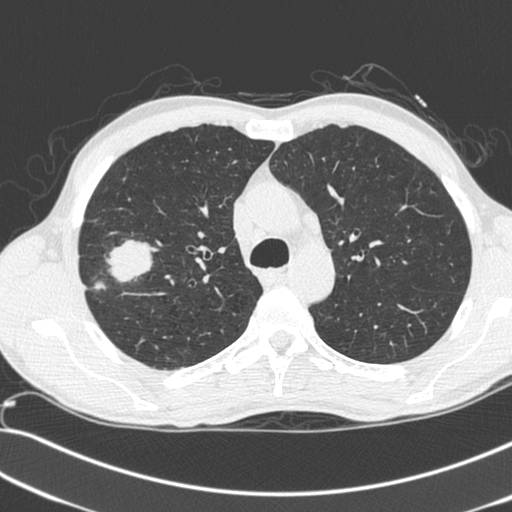
Axial slice from a low-dose chest CT screening exam; first (baseline) screen; lung window (W 1500 / L -600 HU); 1.3 mm slice thickness; standard (soft-tissue) reconstruction kernel (C); 120 kVp; 512 × 512 image matrix. Male, age 55 years at enrolment.
Expert-annotated lung lesion, bounding box [x1, y1, x2, y2] px = [72, 235, 151, 307]. The exam's reader record, not a measurement of the box and not confirmed to be the same lesion: non-calcified nodule or mass ≥4 mm, right upper lobe, 52 × 39 mm, spiculated (stellate) margins, soft tissue attenuation. Official screen result: positive, change unspecified: nodule(s) >= 4 mm or enlarging nodule(s), mass(es), or other non-specific abnormalities suspicious for lung cancer.